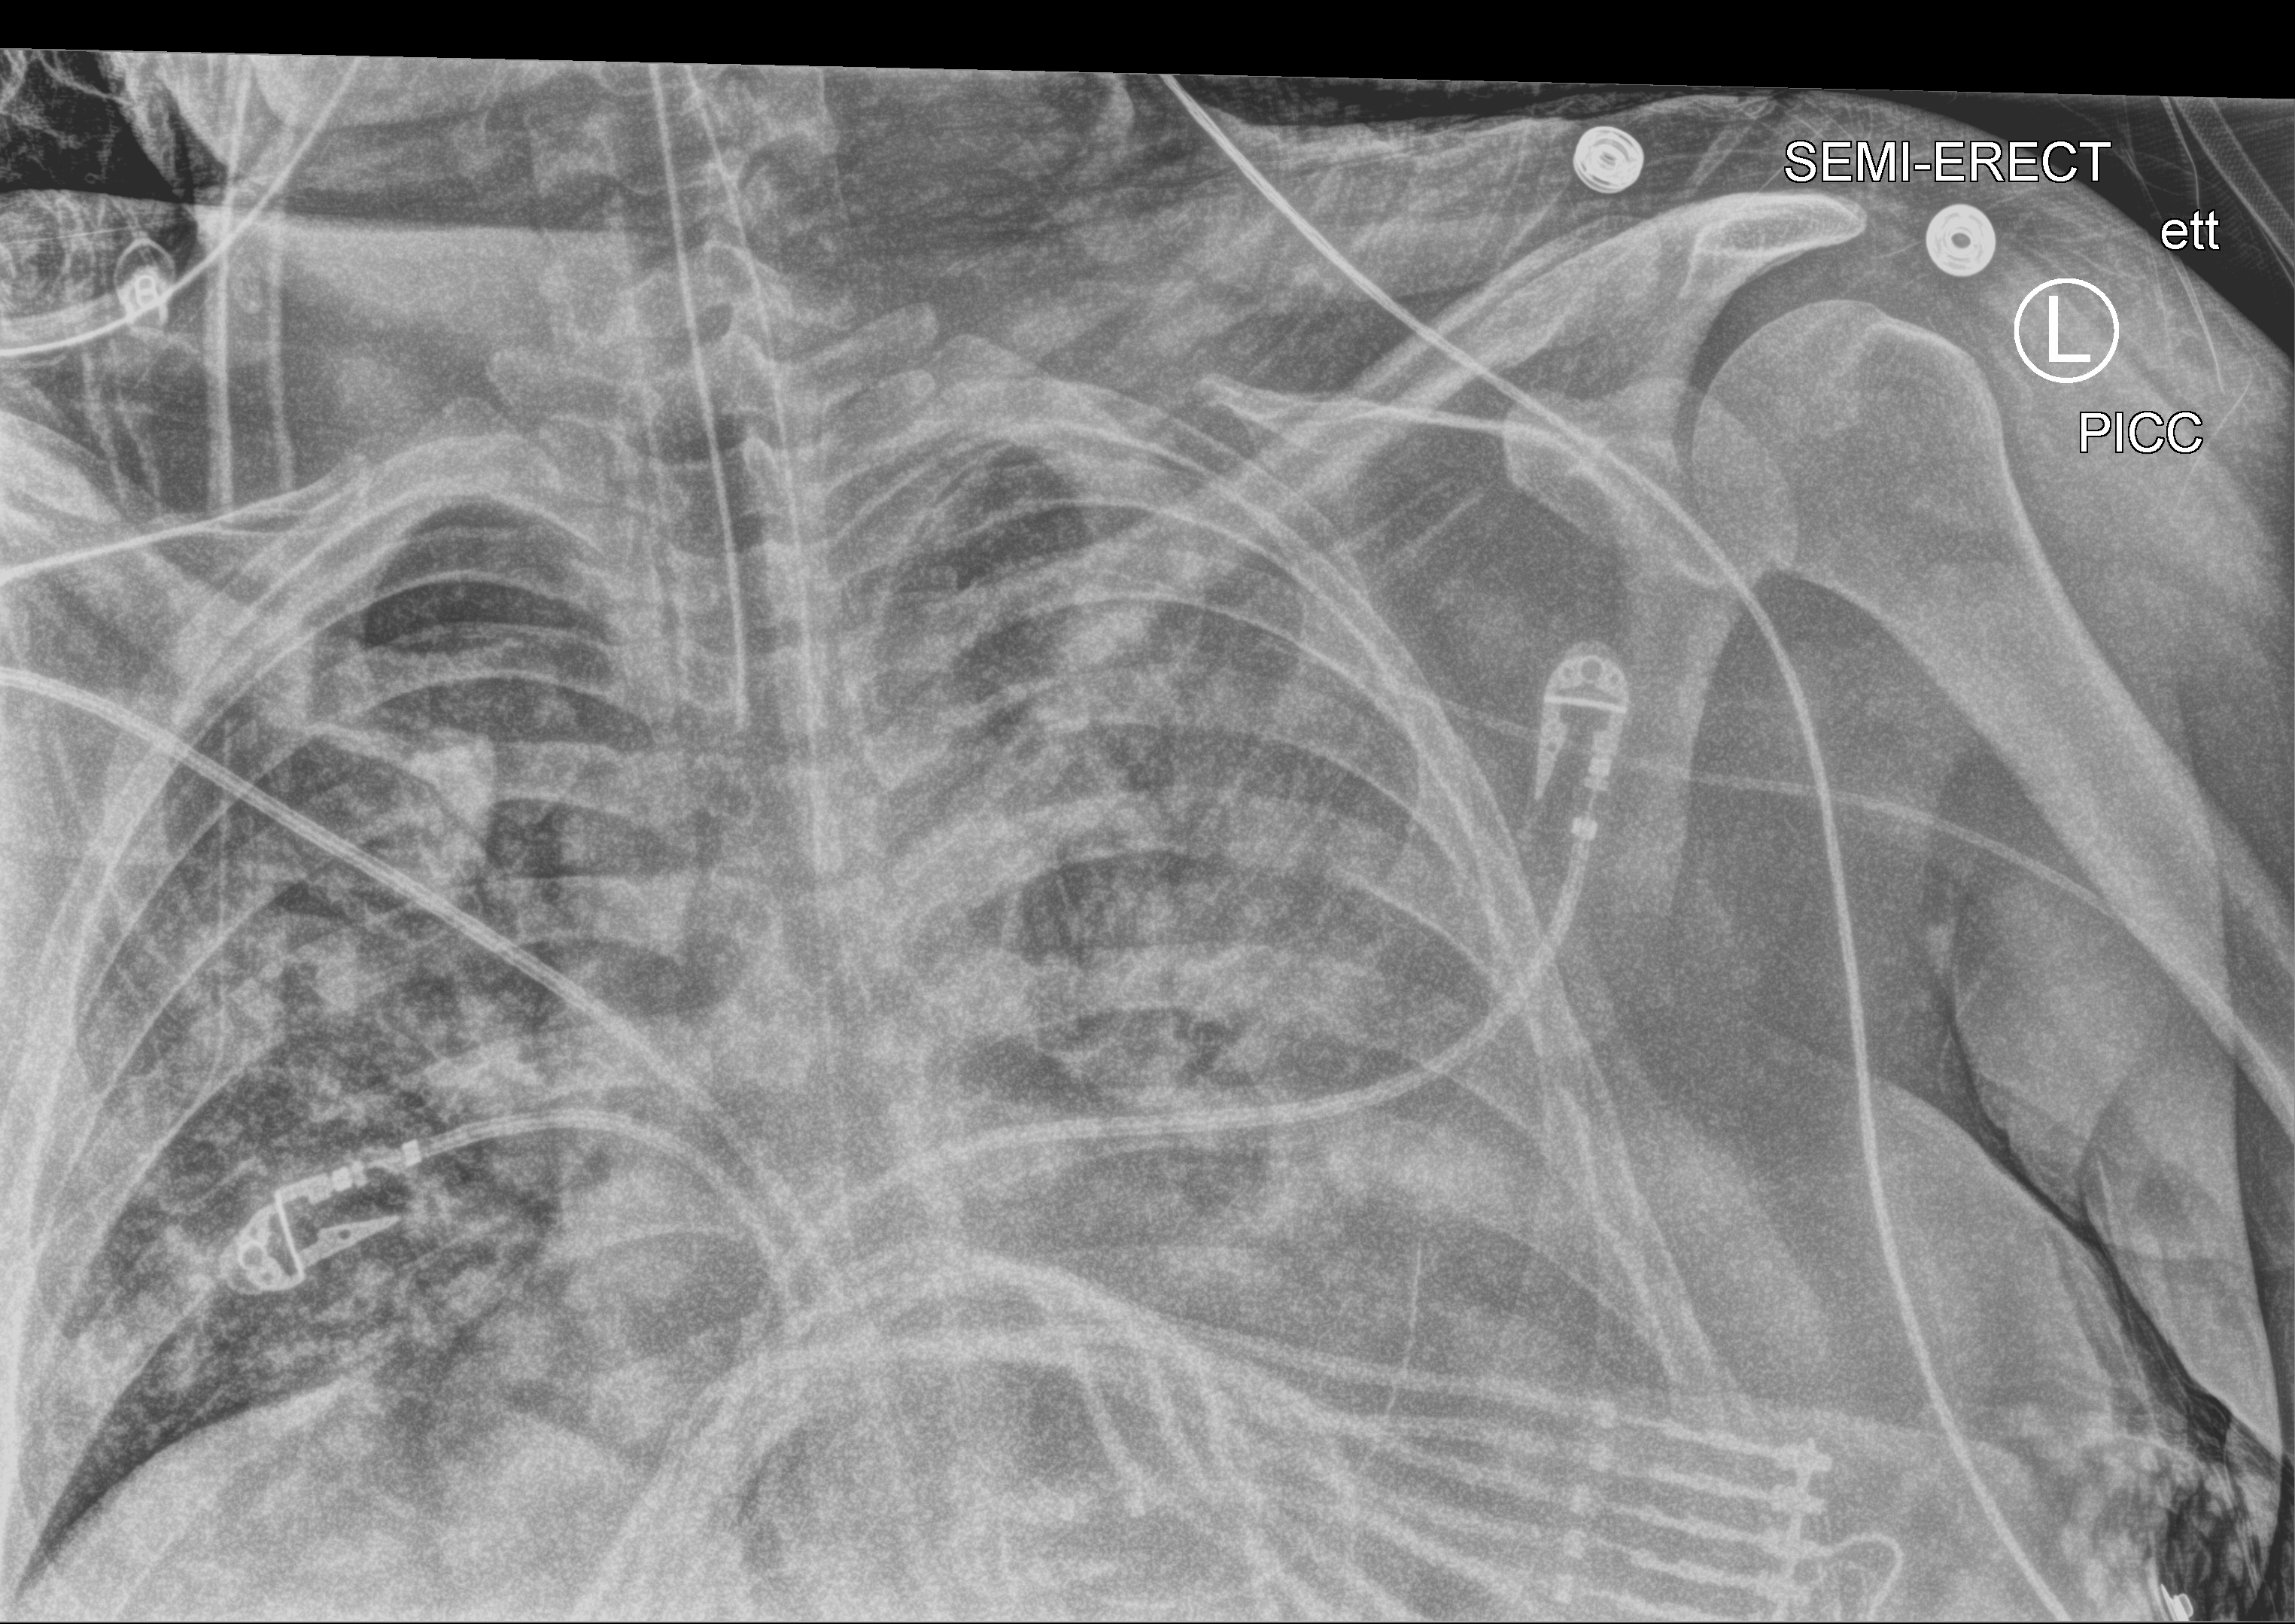
Bedside chest radiograph (computed radiography), anteroposterior (AP) projection. Patient hospitalised with COVID-19, aged 18–59 years.
Hospital-stay facts (about this admission, not read from this image; timing relative to this image not recorded): smoking status (admission record): never; admitted to intensive care during this hospital stay: yes.